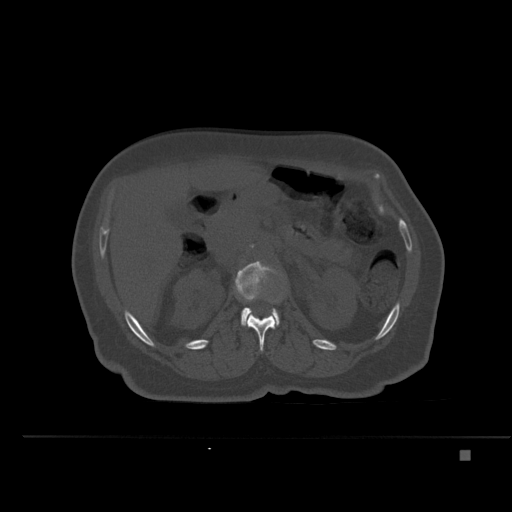
CT including the spine, one axial slice. Position 229 of 477 along the scan axis. Bone window (W 1800 / L 400 HU). 1.5 mm slice thickness. 512 × 512 image matrix. Patient: female, 74 years. From the clinical record (not read from this slice): primary cancer: colon.
Structures marked on this image (semi-automatically segmented with operator editing):
- L1 vertebra: bounding box [x1, y1, x2, y2] px = [247, 301, 277, 351]
- L2 vertebra: [235, 261, 280, 326]